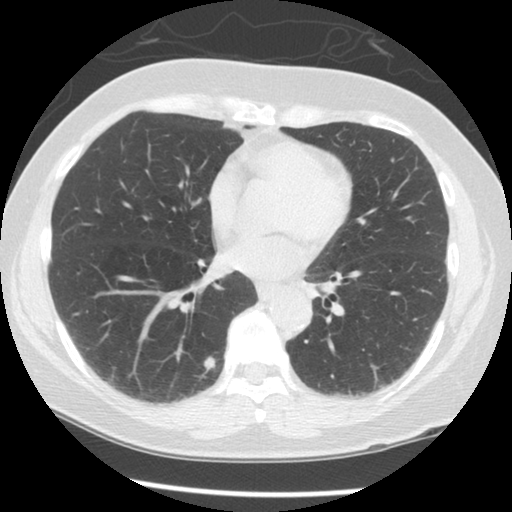
Low-dose screening chest CT, one axial slice; position 59 of 125 along the scan axis; 120 kVp; lung window (W 1500 / L -600 HU); 2.5 mm slice thickness; 512 × 512 image matrix, field of view 331 × 331 mm.
Structures marked on this image (outlined manually by an expert reader):
- lesion 1 (tumor, lower lobe of right lung): box from (x=204, y=356) to (x=216, y=373) px